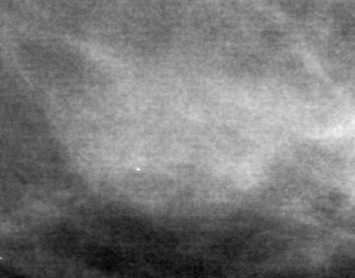
Region of interest cut from a scanned film mammogram (one marked finding), right breast, MLO view.
Mass, shape lobulated, margins circumscribed; BI-RADS assessment category 3; pathology (as recorded): benign.